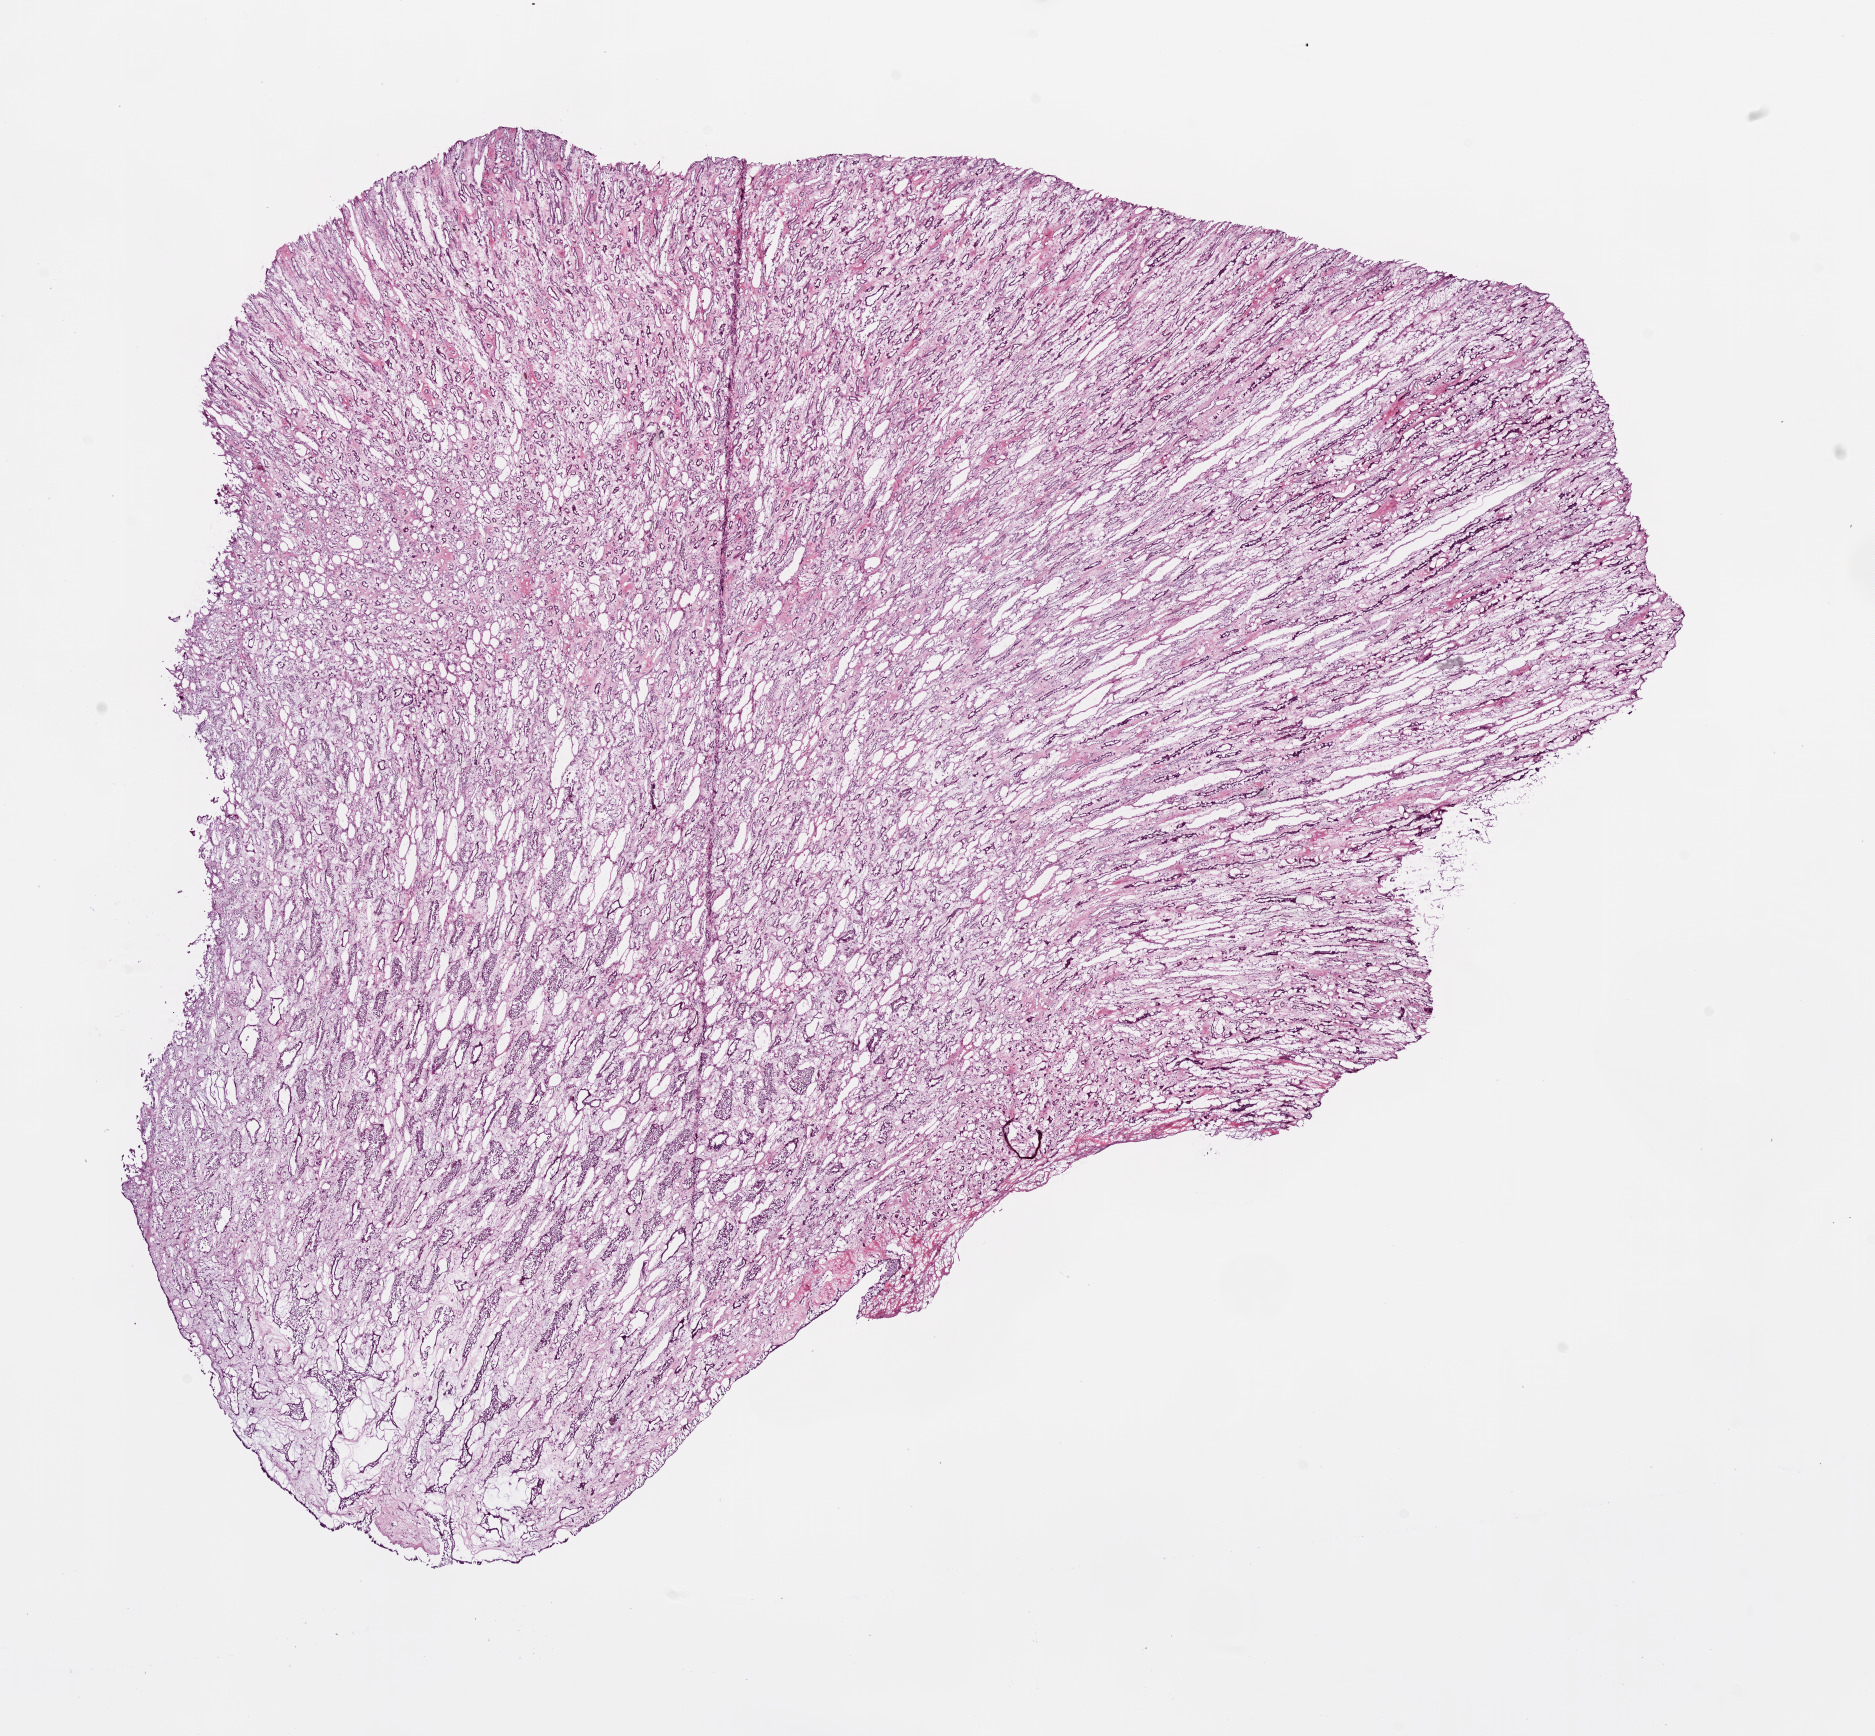
Digitized H&E tissue section (whole slide), whole scanned area (about 15.0 x 13.9 mm, acquisition: 20x scan) shown as a low-resolution overview; frozen section from the bottom of the tissue portion; kidney, solid tissue normal (non-tumour tissue) sample. Female, age 62 years at initial diagnosis.
This section: solid tissue normal sample (biorepository sample class). Patient diagnosis: Clear cell adenocarcinoma, NOS.